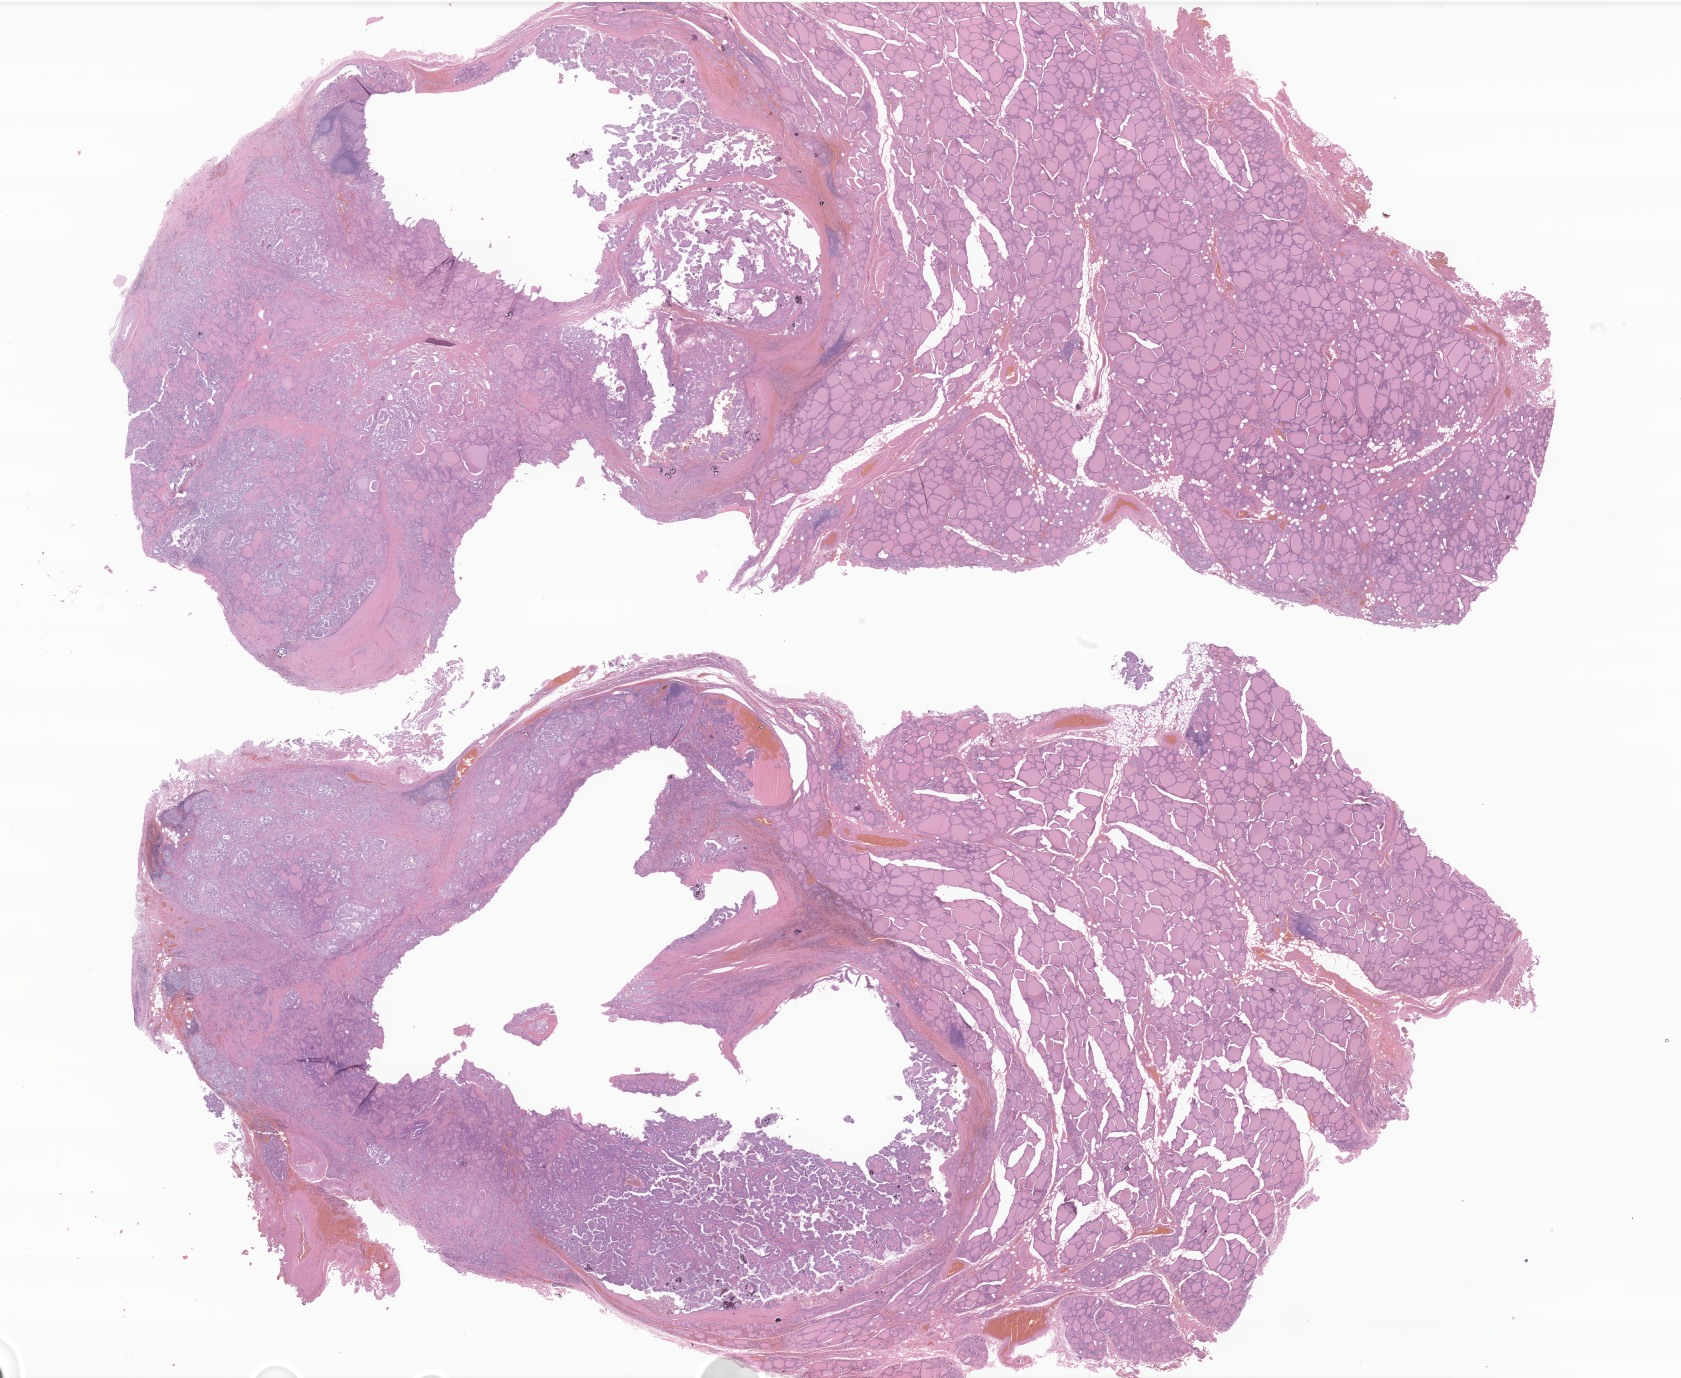
H&E whole-slide image of tumor tissue from the thyroid — a low-resolution overview of the entire scanned area, about 28.3 x 23.2 mm. Formalin-fixed, paraffin-embedded (FFPE) tissue. Male patient, age 239 months.
* diagnosis (ICD-O-3 morphology term): Papillary carcinoma, NOS